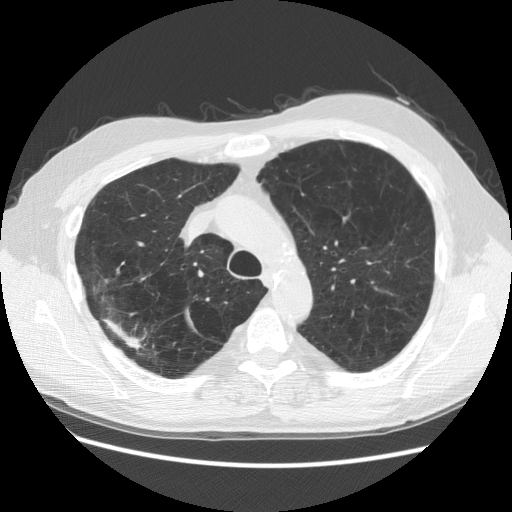
Low-dose screening chest CT, one axial slice. Slice 100 of 137 in the series (ordered by position). Reconstruction kernel STANDARD. 140 kVp. Lung window (W 1500 / L -600 HU). 2.5 mm slice thickness. 512 × 512 image matrix.
Annotated regions visible in this slice (expert manual segmentation):
- lesion 2 (nodule, upper lobe of right lung): box from (x=104, y=317) to (x=144, y=350) px